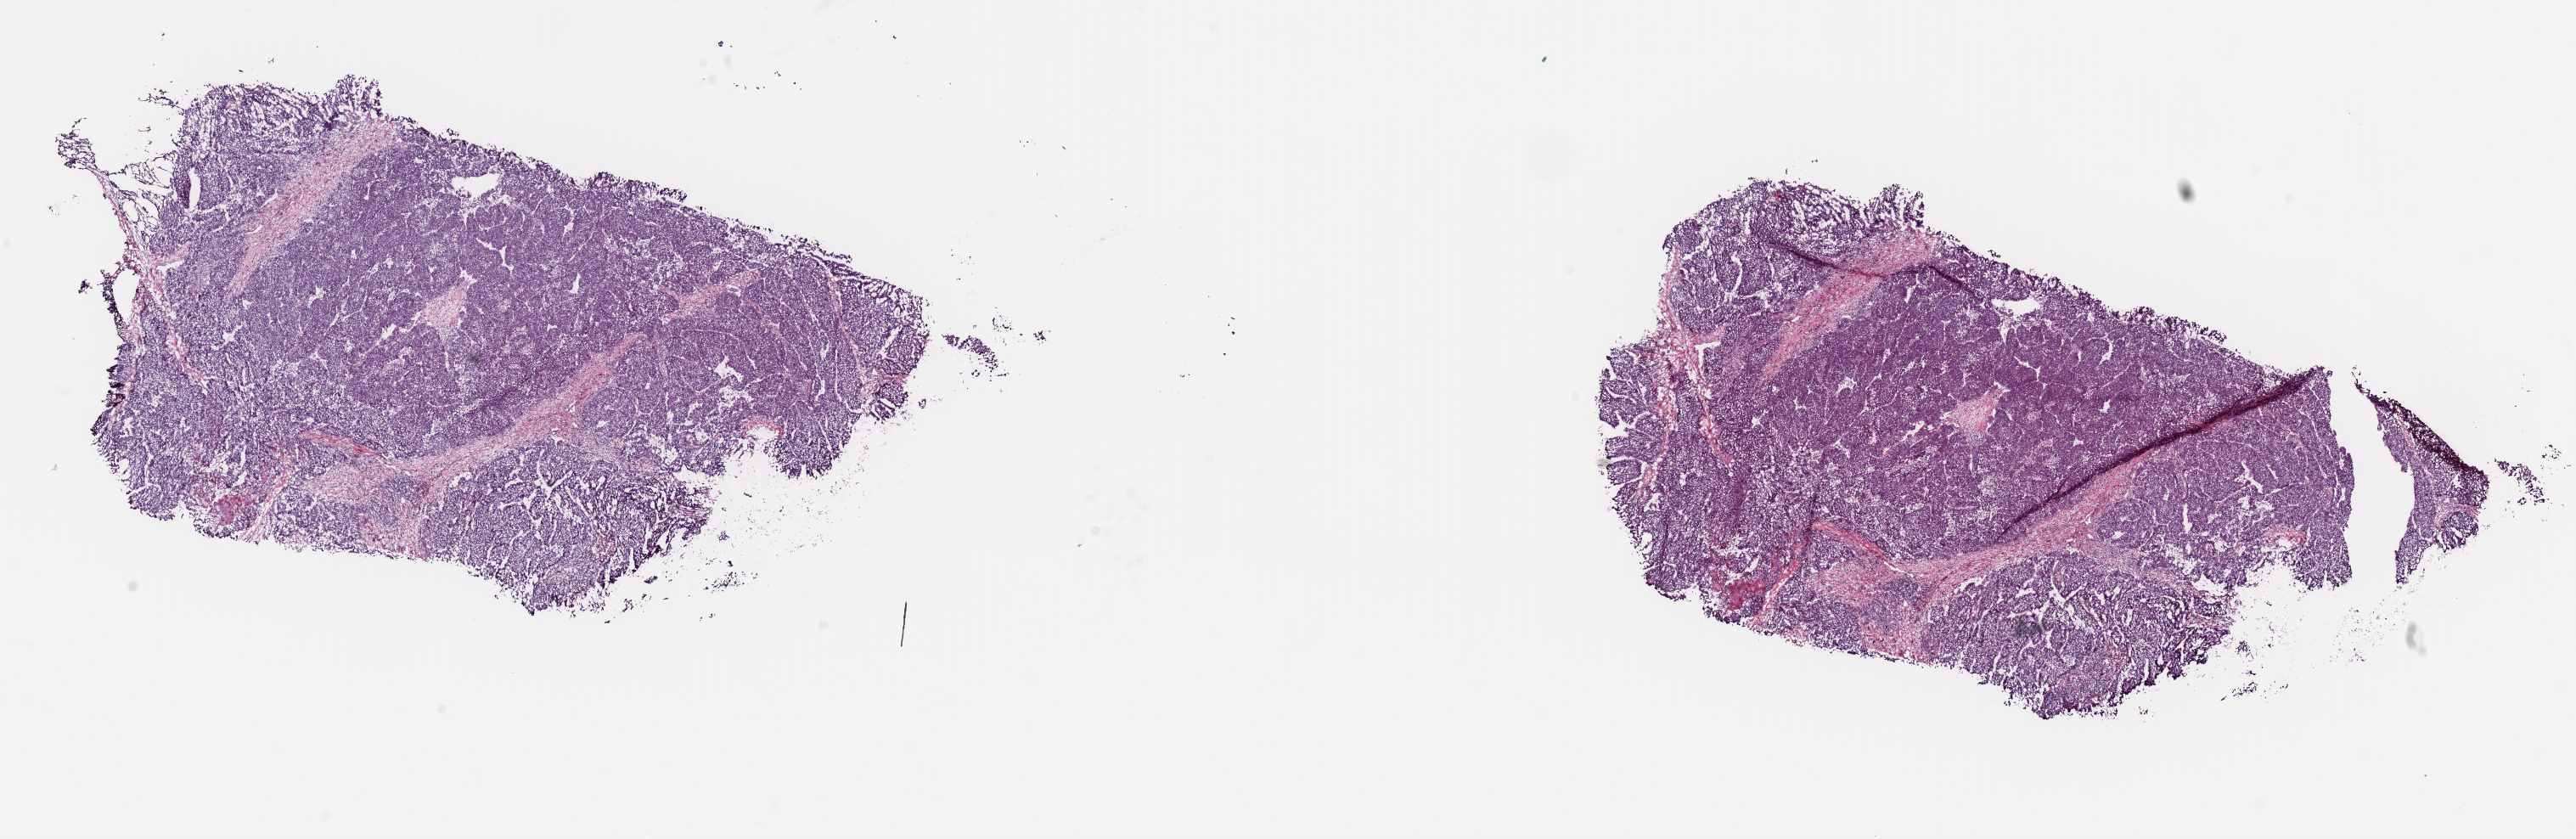
Digitized H&E tissue section (whole slide) — whole scanned area (about 24.0 x 7.8 mm, slide scanned at 40x) shown as a low-resolution overview, frozen section from the top of the tissue portion, primary tumour sample from the liver. Patient: female, age at initial diagnosis 52 years. Histologic grade: G3 (poorly differentiated). Pathologist review of this section (percent, as recorded): tumour cells 95%, tumour nuclei 92%, normal cells 0%, stromal cells 5%, necrosis 0%. Inflammatory infiltration, as recorded: lymphocyte infiltration 0%, monocyte infiltration 0%, neutrophil infiltration 0%.
- AJCC pathologic stage: IIIA (7th edition)
- pathologic diagnosis: Hepatocellular carcinoma, NOS